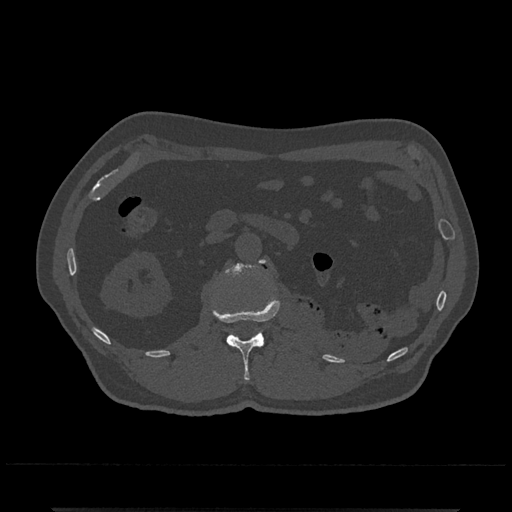
CT including the spine, one axial slice; position 341 of 797 along the scan axis; reconstruction kernel Br40s/3; 120 kVp; bone window (W 1800 / L 400 HU); 512 × 512 image matrix. Patient: male, 67 years. Case-level facts recorded for this patient, not image findings: primary cancer: prostate.
Outlined on this slice (semi-automatic segmentation, software-assisted and operator-edited):
- L1 vertebra: bounding box [x1, y1, x2, y2] px = [213, 299, 280, 381]
- L2 vertebra: [225, 259, 267, 276]